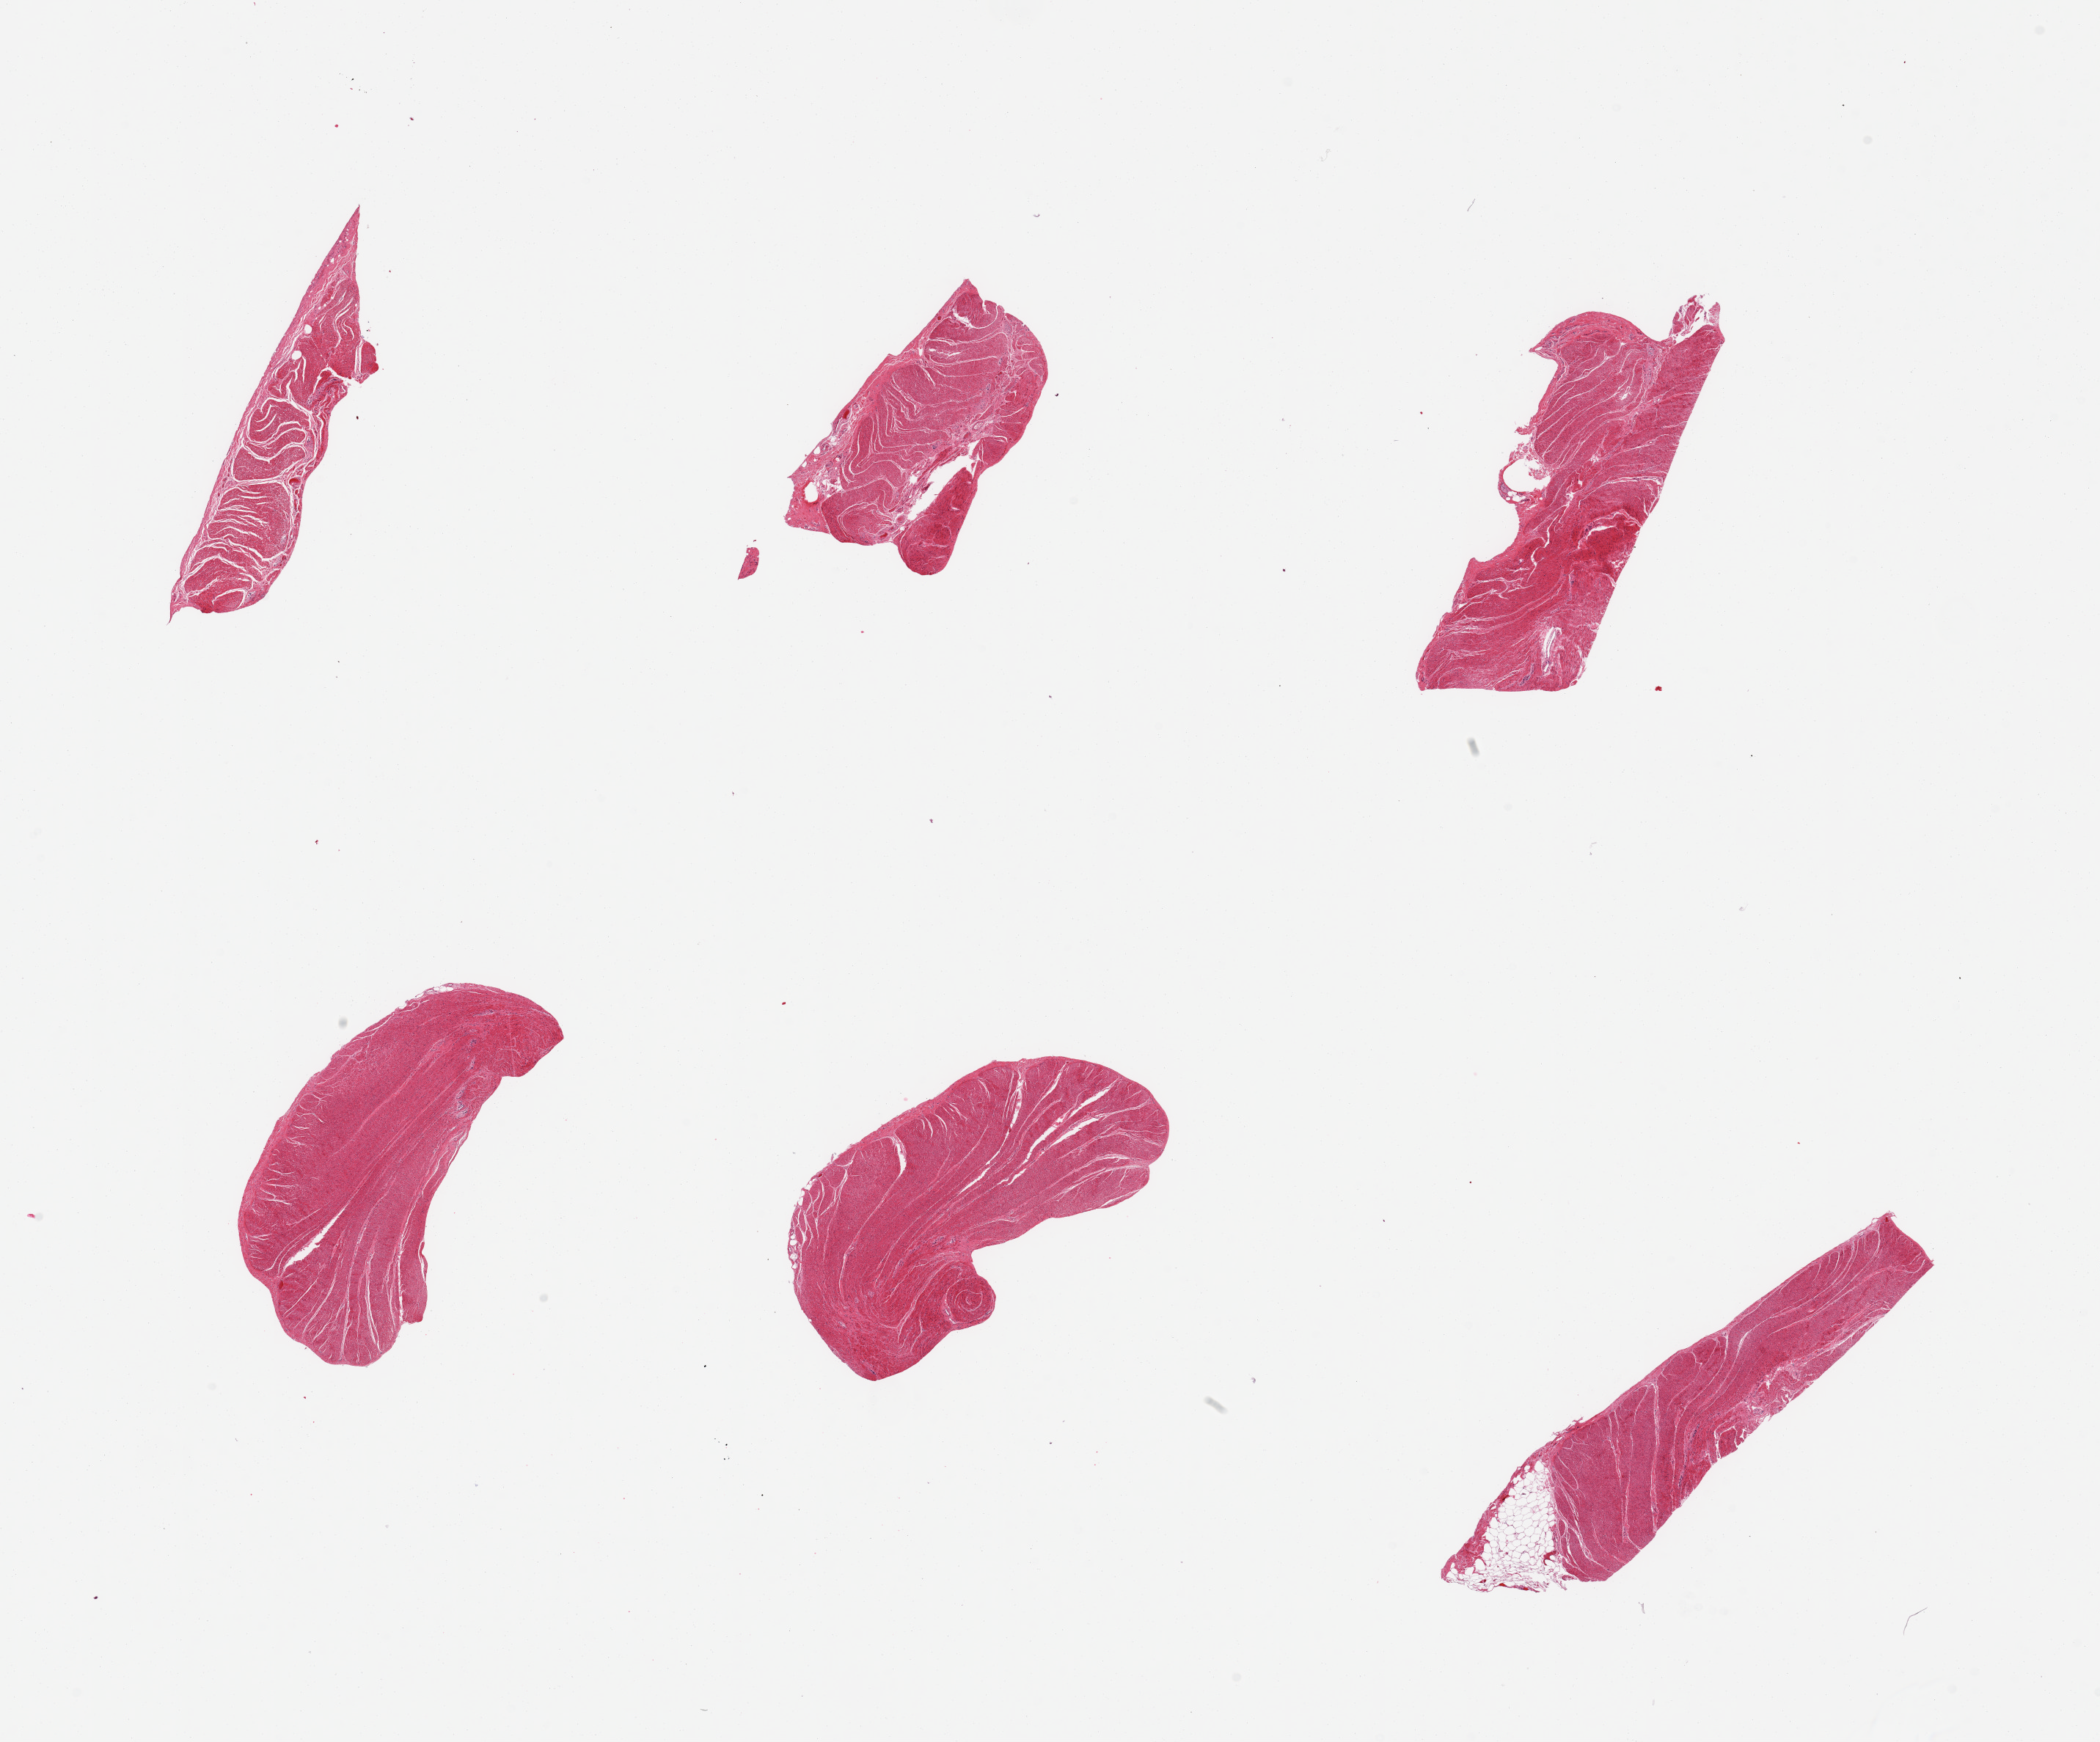
Digitized H&E-stained section — low-resolution overview of the scanned area, about 22.6 x 18.8 mm; PAXgene-fixed, paraffin-embedded tissue; section of sigmoid colon (target tissue); tissue donor sample. Donor sex: male.
Reviewer comment on this tissue sample: 6 pieces, confirmed target muscularis.